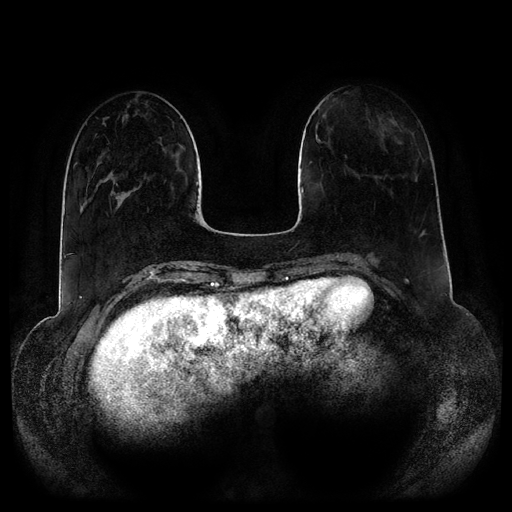
Breast MRI (dynamic contrast-enhanced, multi-phase), one axial slice. Slice 34 of 116 in the series (ordered by position). Dynamic contrast-enhanced series, time point 2 of 5 at this slice position (early post-contrast). 1.5 T. TE 2.5 ms, TR 5.2 ms. 2 mm slice thickness. 512 × 512 image matrix, field of view 390 × 390 mm. Female patient, age 34 years.
Structures marked on this image (semi-automatic segmentation, software-assisted and operator-edited):
- breast lesion (labelled benign in the annotation): bounding box <316,134,324,147> (left, top, right, bottom; pixels)